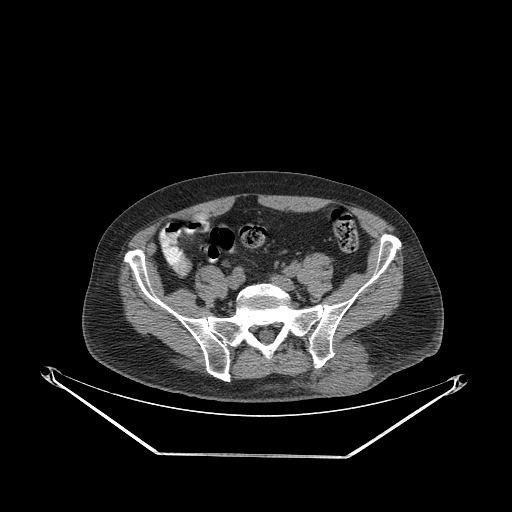
CT of an extremity soft-tissue mass (from a PET/CT study), one axial slice; position 80 of 267 along the scan axis; reconstruction kernel STANDARD; 140 kVp; soft-tissue window (W 400 / L 40 HU); 3.75 mm slice thickness; 512 × 512 image matrix, field of view 500 × 500 mm. Male patient. Case-level facts recorded for this patient, not image findings: histological type: leiomyosarcoma; grade: intermediate; site of the primary tumour: left pelvis.
Annotated regions visible in this slice (expert contour drawn on MRI and transferred to this co-registered scan by the dataset authors):
- gross tumour volume (mass): bounding box (x1, y1, x2, y2) in pixels: (311, 343, 371, 396)